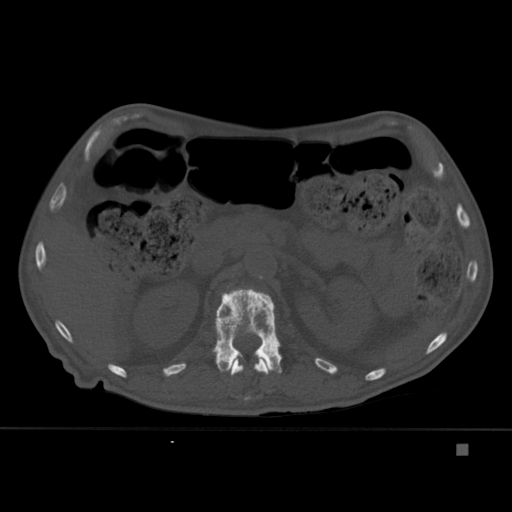
CT including the spine, one axial slice. Position 186 of 451 along the scan axis. Bone window (W 1800 / L 400 HU). 1.5 mm slice thickness. 512 × 512 image matrix, field of view 378 × 378 mm. Patient: male, 75 years. From the clinical record (not read from this slice): primary cancer: prostate.
Outlined on this slice (semi-automatically segmented with operator editing):
- L1 vertebra: bounding box [x1, y1, x2, y2] px = [212, 288, 282, 373]
- T12 vertebra: [230, 355, 269, 400]